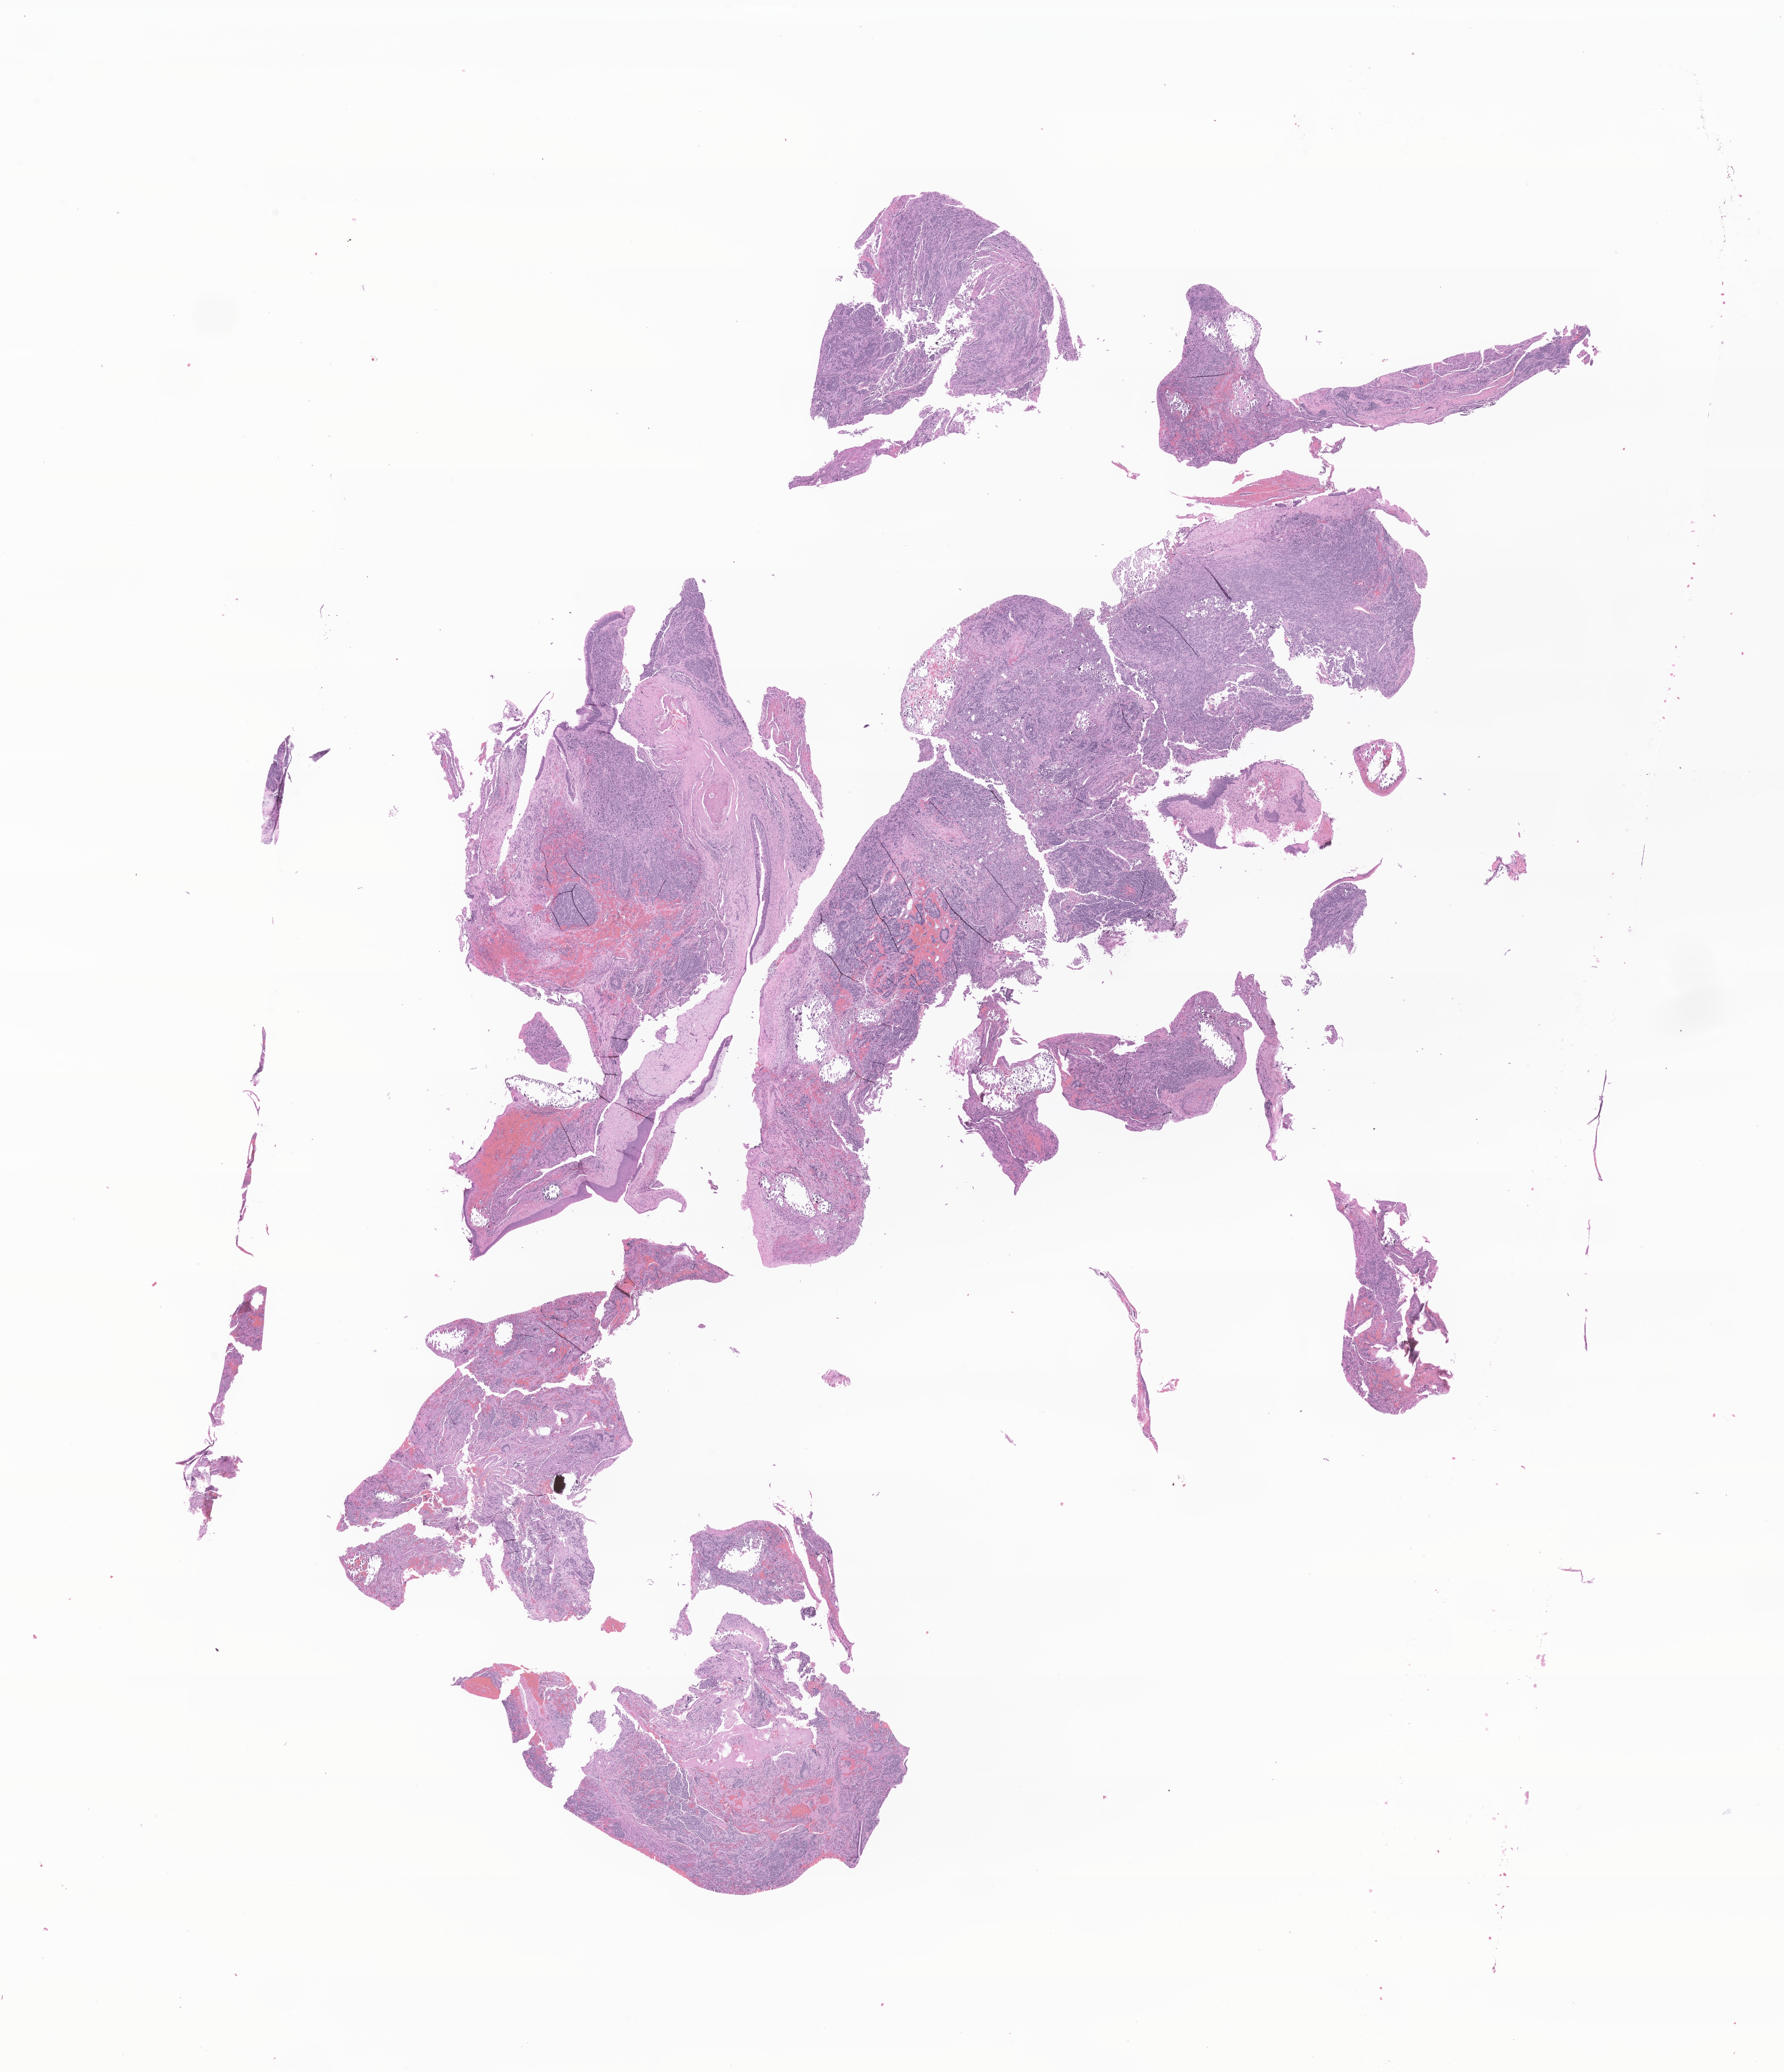
Hematoxylin and eosin (H&E) whole-slide image of tumor tissue from the nasal cavity, whole scanned area (about 18.9 x 22.0 mm) shown as a low-resolution overview, formalin-fixed, paraffin-embedded (FFPE) tissue. Patient: female, age 201 months (16 years 9 months).
Diagnosis (ICD-O-3 morphology term): Olfactory neuroblastoma.